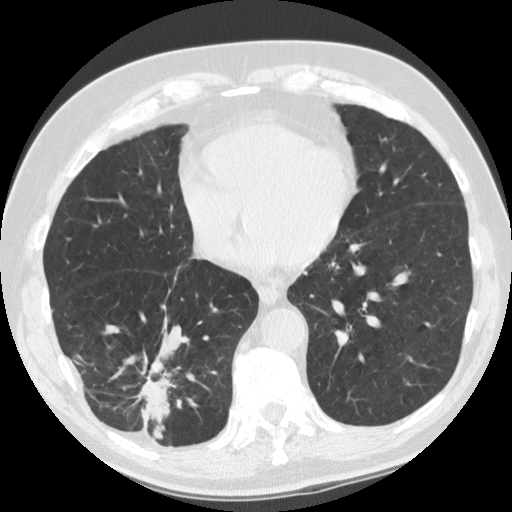
Low-dose screening chest CT, one axial slice. Reconstruction kernel STANDARD. 120 kVp. Lung window (W 1500 / L -600 HU). 2.5 mm slice thickness. 512 × 512 image matrix, field of view 340 × 340 mm.
Structures marked on this image (expert manual segmentation):
- lesion 1 (tumor, lower lobe of right lung): box from (x=137, y=361) to (x=179, y=439) px